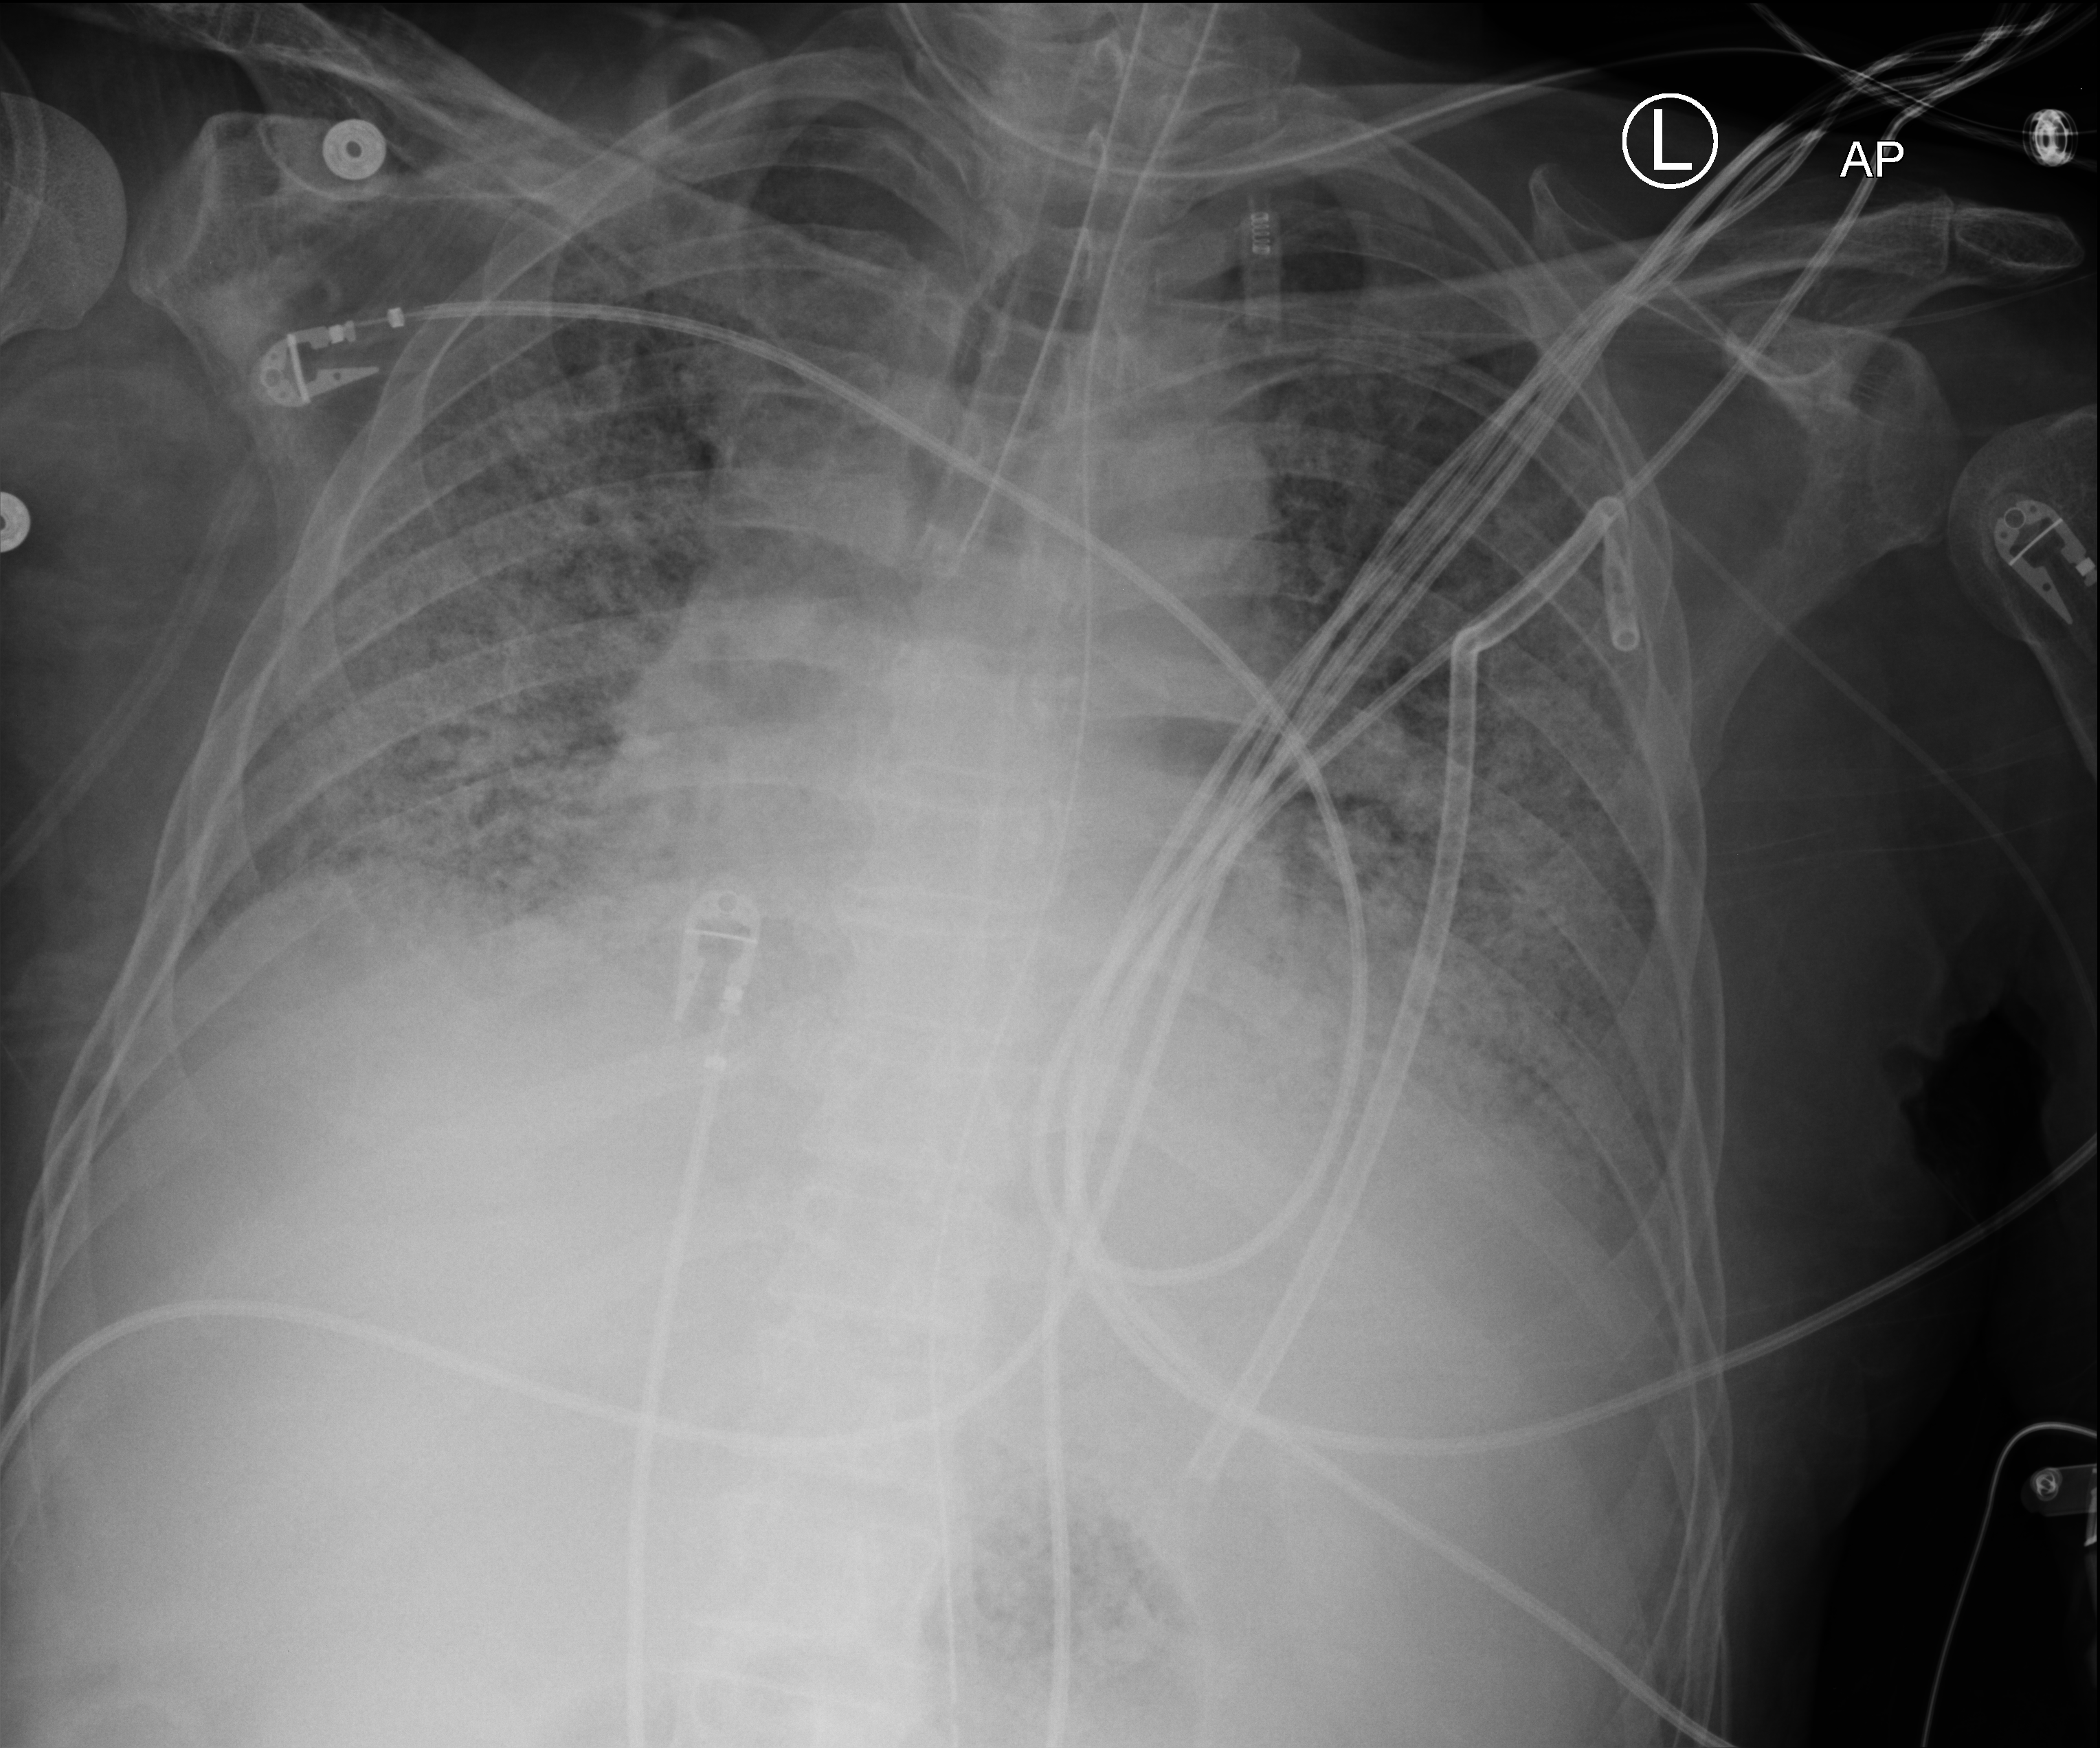
Portable chest radiograph. Male patient hospitalised with COVID-19, age 60–74 years.
Hospital-stay facts (about this admission, not read from this image; timing relative to this image not recorded): length of hospital stay: 54 days; admitted to intensive care during this hospital stay: yes; mechanically ventilated during this hospital stay: yes.